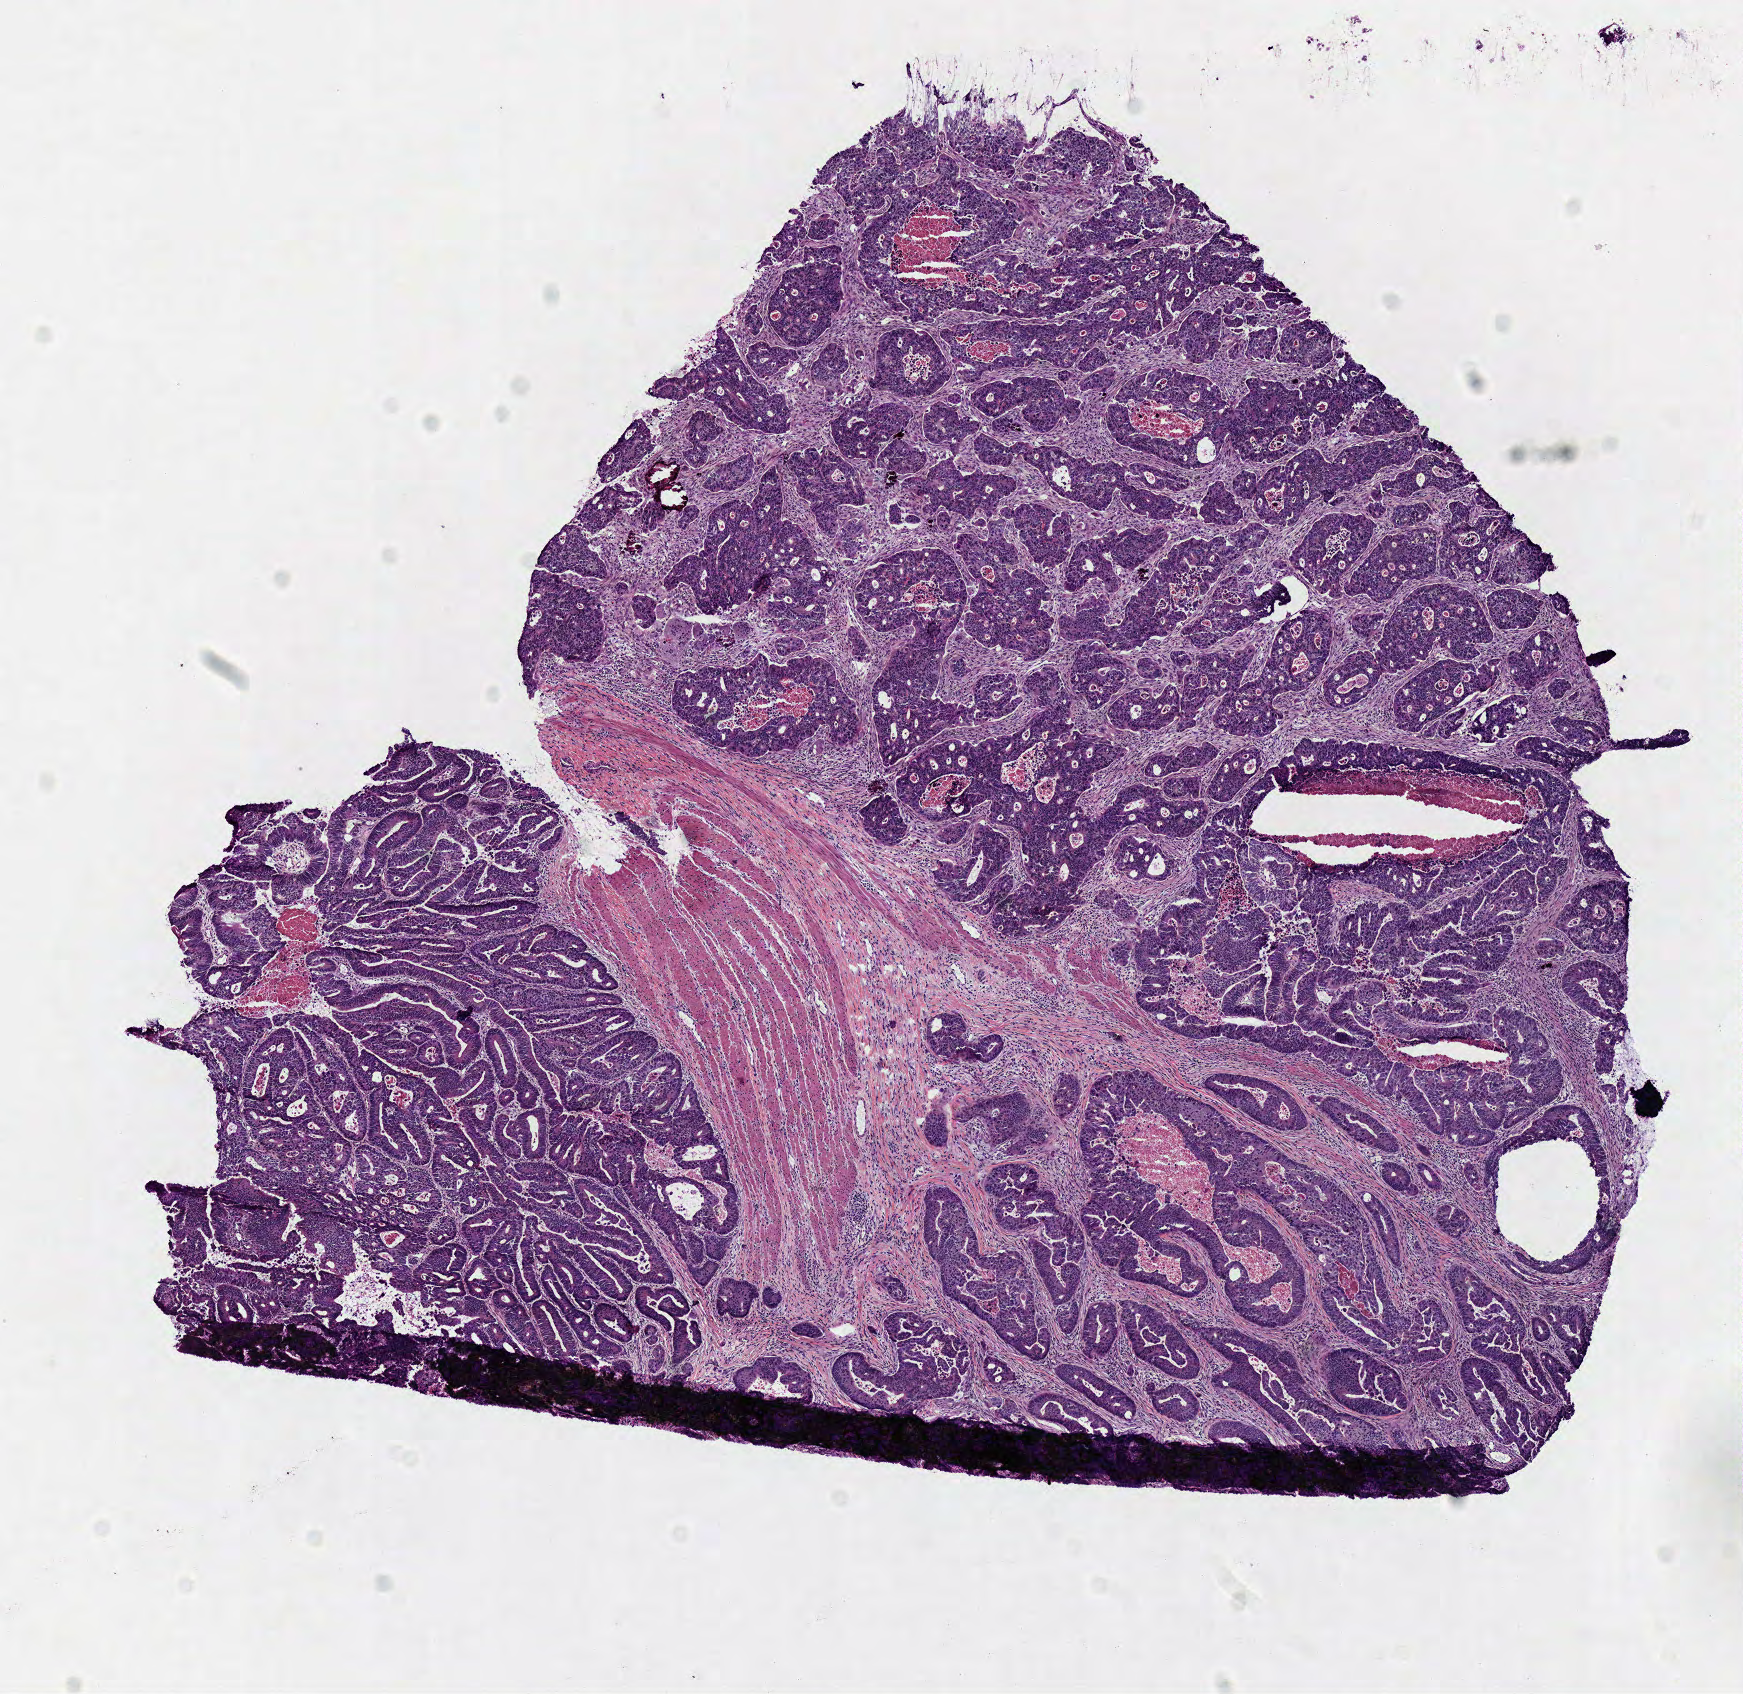
H&E whole-slide image — whole scanned area (about 6.9 x 6.7 mm, from a 40x scan) shown as a low-resolution overview. Frozen section. Primary tumour sample from the colon. Female patient; age at initial diagnosis 54 years. Pathologist review of this section (percent, as recorded): tumour cells 67%, tumour nuclei 80%, normal cells 0%, stromal cells 25%, necrosis 8%.
Lymph nodes positive (case pathology): 1 of 25 examined. AJCC pathologic stage: IV (6th edition). Diagnosis: Adenocarcinoma, NOS (sigmoid colon).